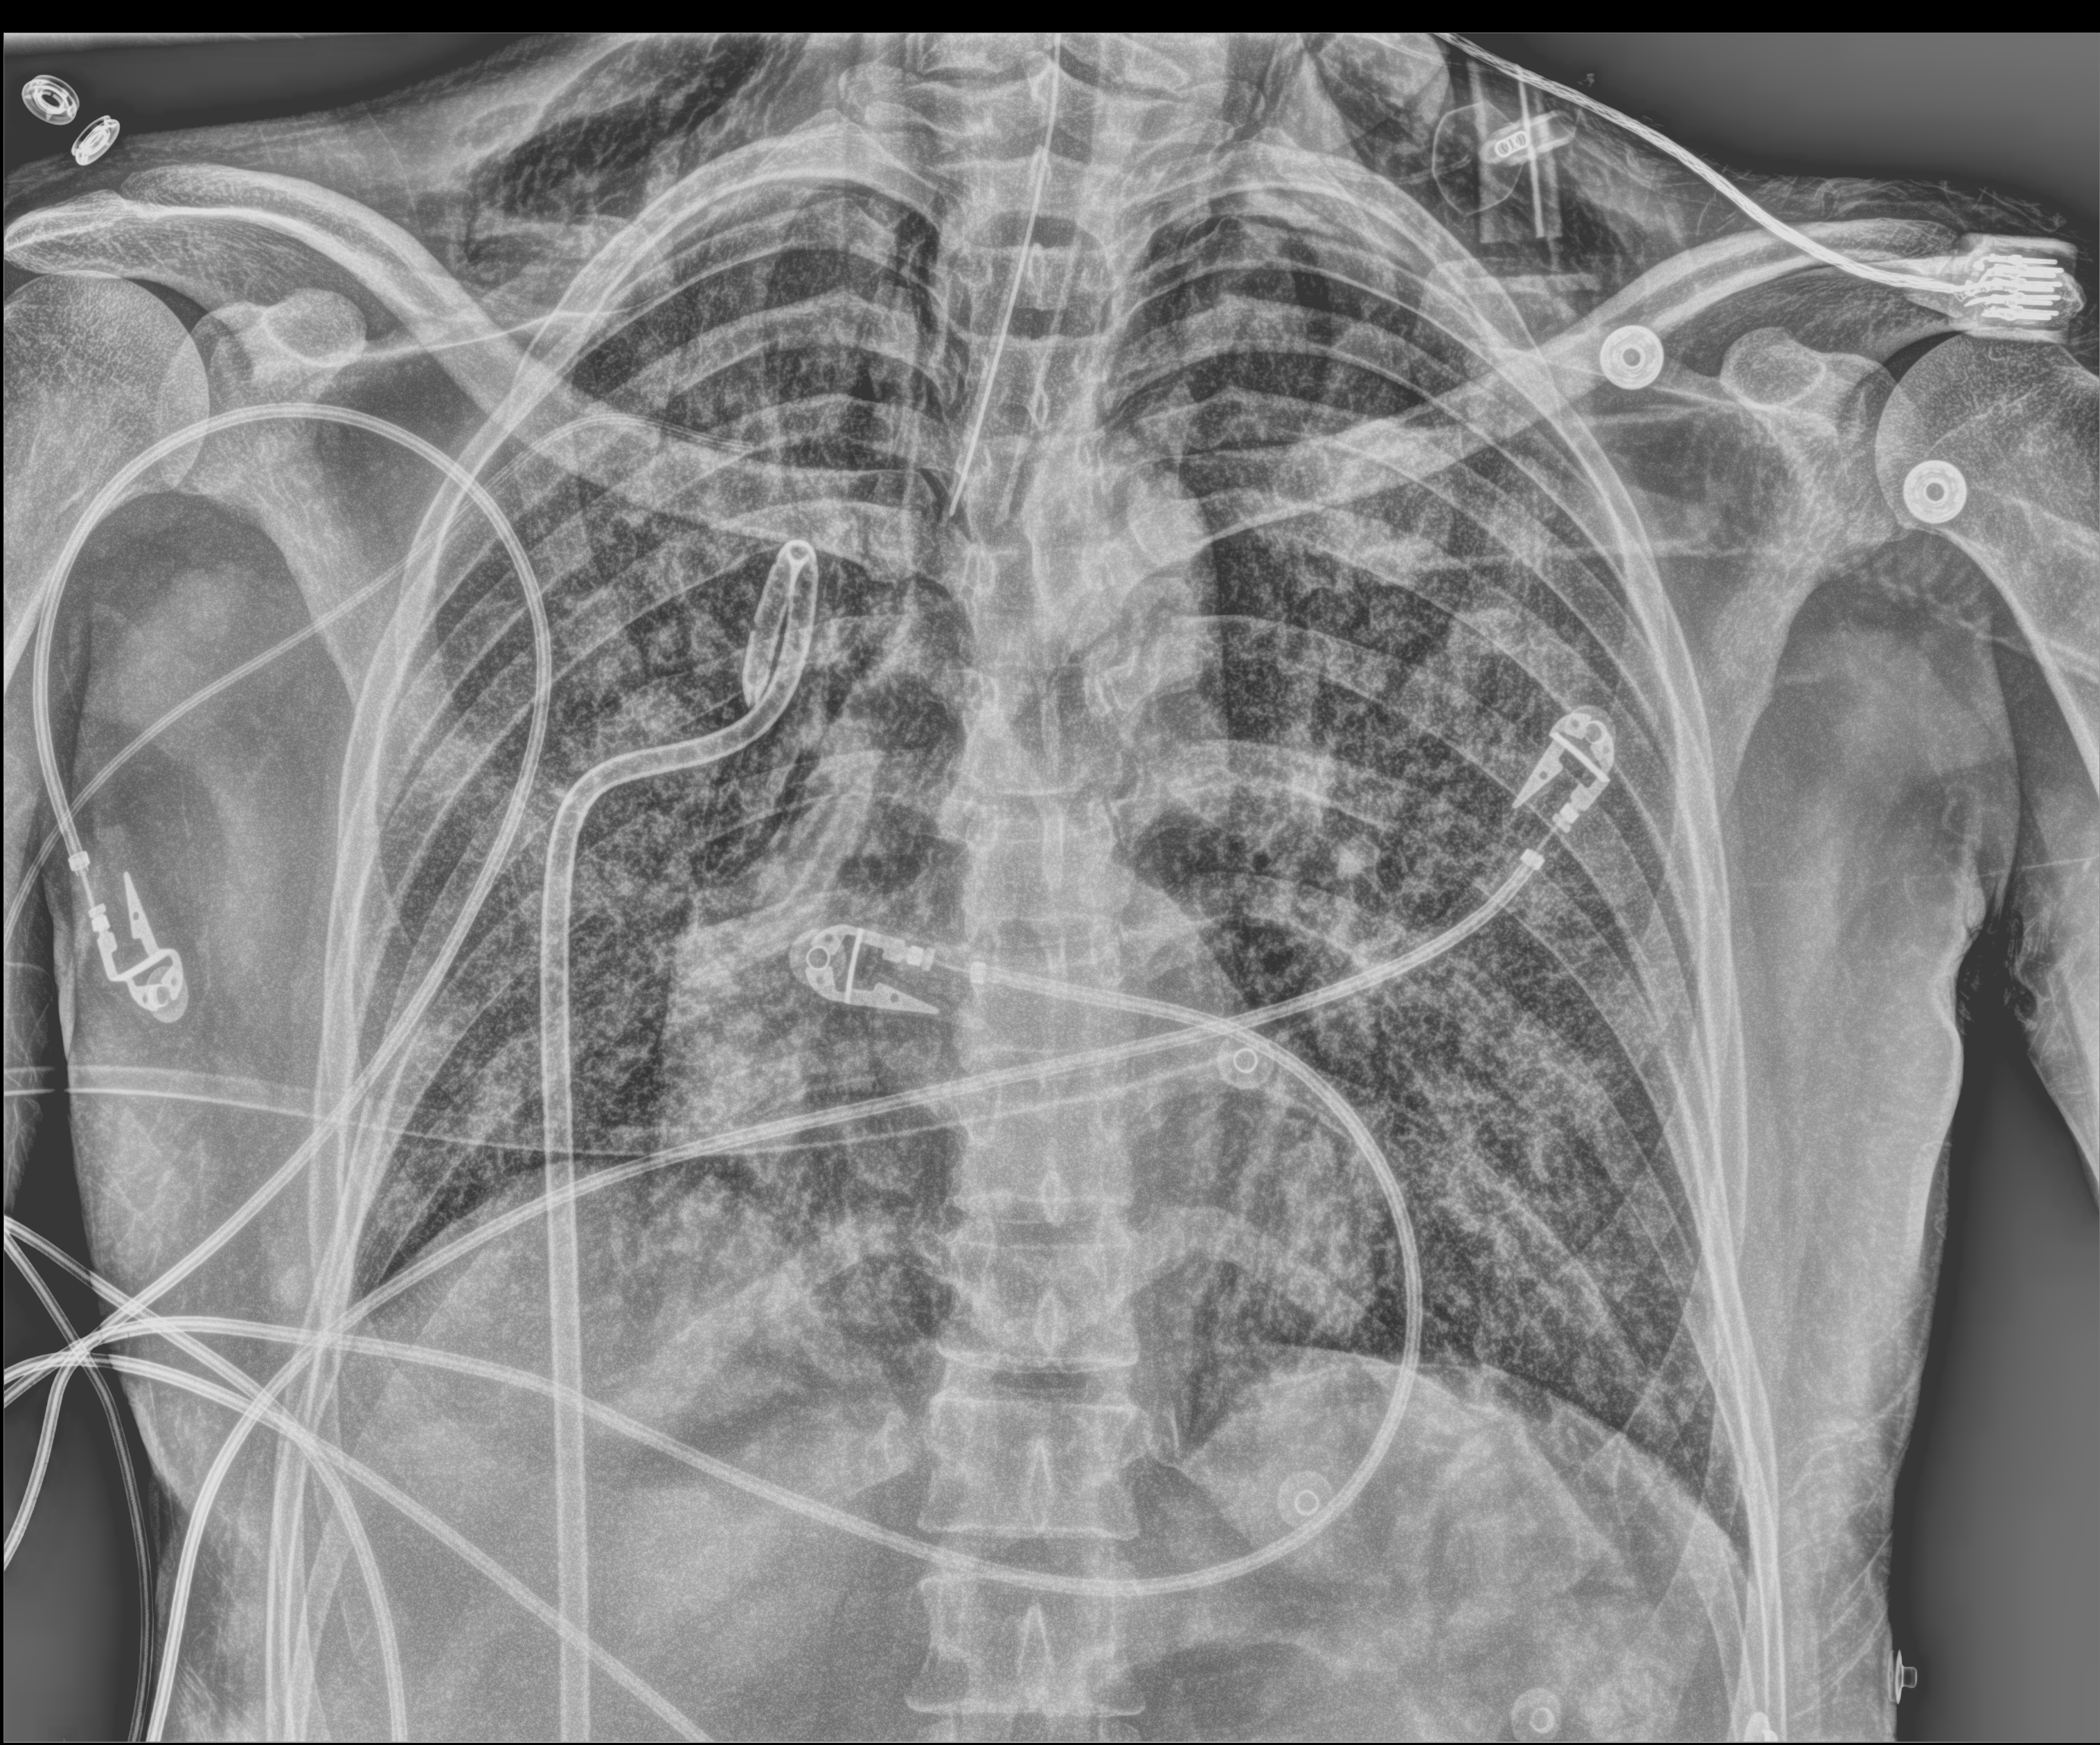
Portable chest radiograph; anteroposterior (AP) projection. Adult patient hospitalised with COVID-19, age 18–59 years.
Hospital-stay facts (about this admission, not read from this image; timing relative to this image not recorded): admitted to intensive care during this hospital stay: yes; length of hospital stay: 41 days.